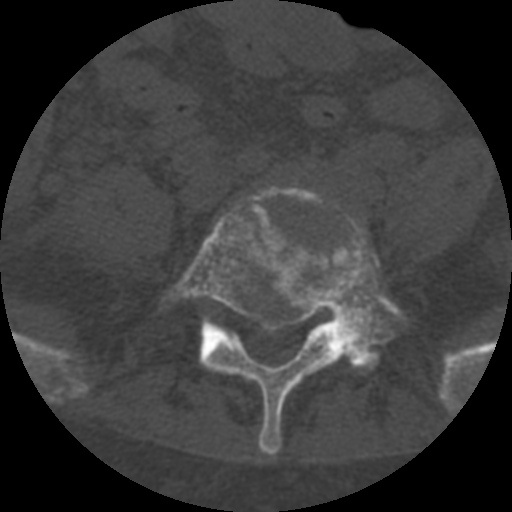
CT including the spine, one axial slice. 120 kVp. One of 3 acquisitions stored at this slice position. Bone window (W 1800 / L 400 HU). 1.25 mm slice thickness. 512 × 512 image matrix, field of view 160 × 160 mm. Patient age 55 years. Case-level facts recorded for this patient, not image findings: primary cancer: colon; vertebrae with lytic lesions (as recorded): T12, L1, L5.
Structures marked on this image (semi-automatic segmentation, software-assisted and operator-edited):
- L5 vertebra: bounding box (x1, y1, x2, y2) in pixels: (160, 187, 415, 456)